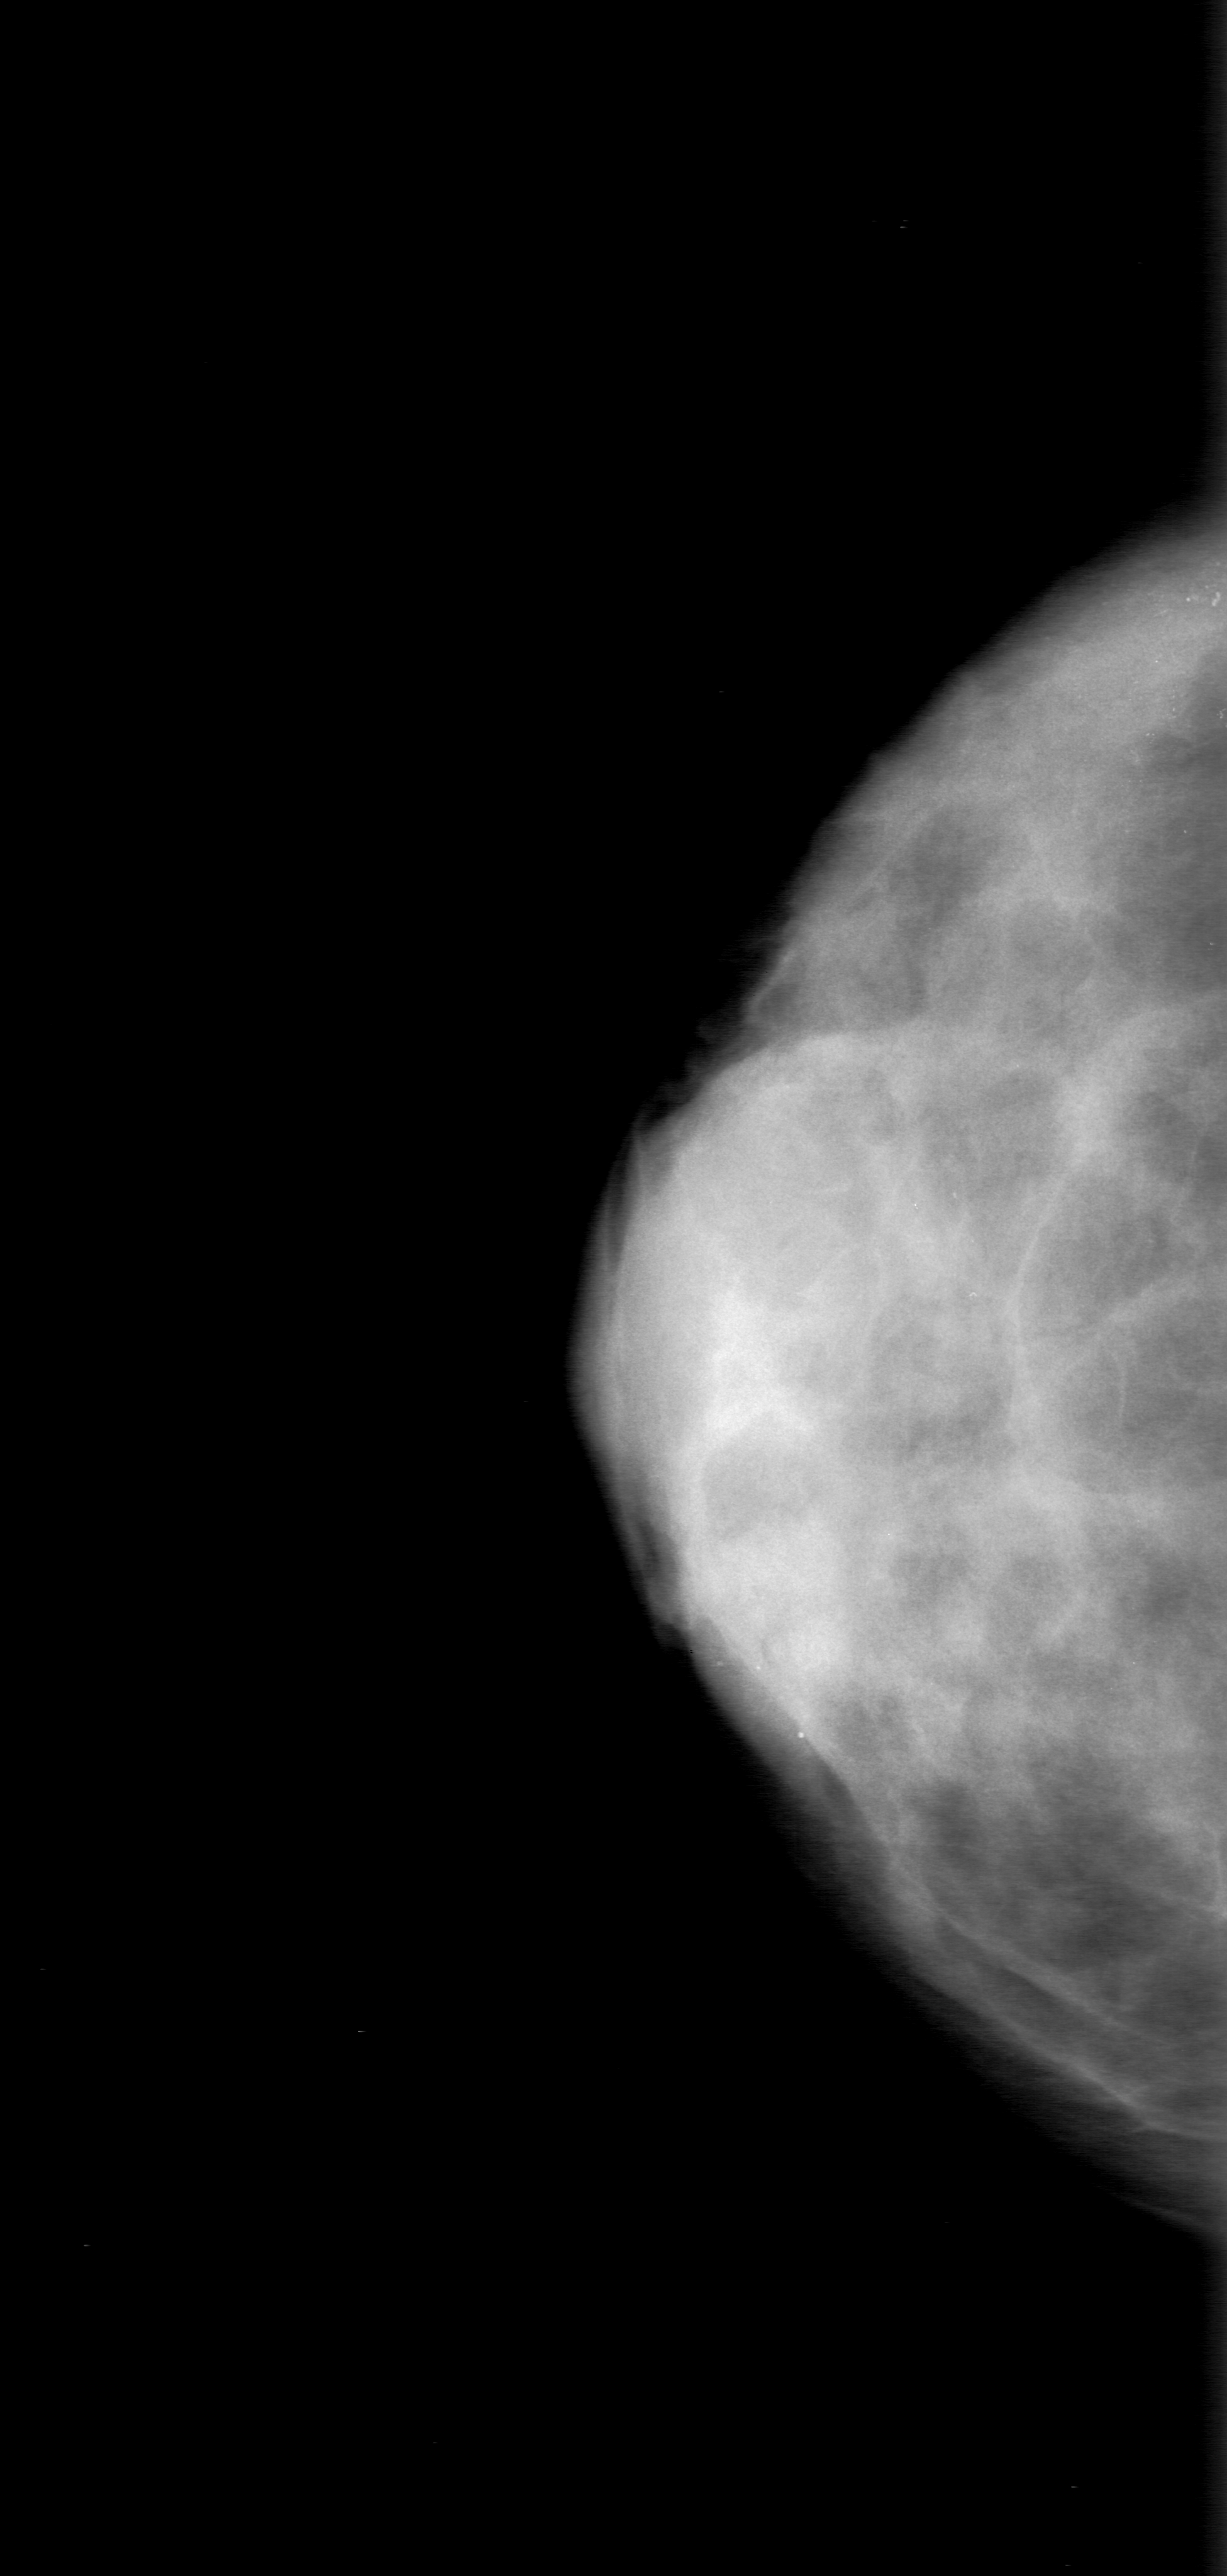
Digitized screen-film mammogram, right breast, CC view, breast composition: extremely dense (BI-RADS density category 4 of 4).
Radiologist-marked abnormalities on this image: calcifications, morphology pleomorphic, distribution clustered; BI-RADS assessment category 3; pathology (as recorded): malignant.